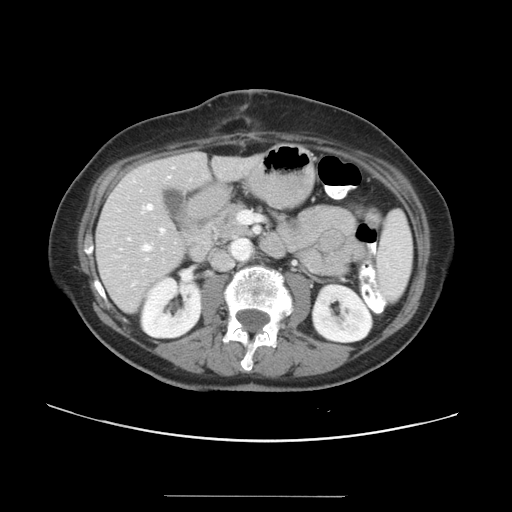
Contrast-enhanced abdominal CT, one axial slice. Position 13 of 34 along the scan axis. Reconstruction kernel STANDARD. 120 kVp. Intravenous contrast given. Soft-tissue window (W 400 / L 40 HU). 512 × 512 image matrix, field of view 382 × 382 mm. Female patient, age 69 years. Case-level facts recorded for this patient, not image findings: diagnosis: colorectal cancer liver metastases, imaged before liver resection; multiple liver metastases: yes.
Outlined on this slice (expert manual segmentation):
- hepatic veins: bounding box <120,176,170,251> (left, top, right, bottom; pixels)
- liver: <97,152,258,311>
- planned liver remnant (the part of the liver to remain after resection): <97,152,258,311>
- portal vein (with intrahepatic branches): <160,211,261,233>